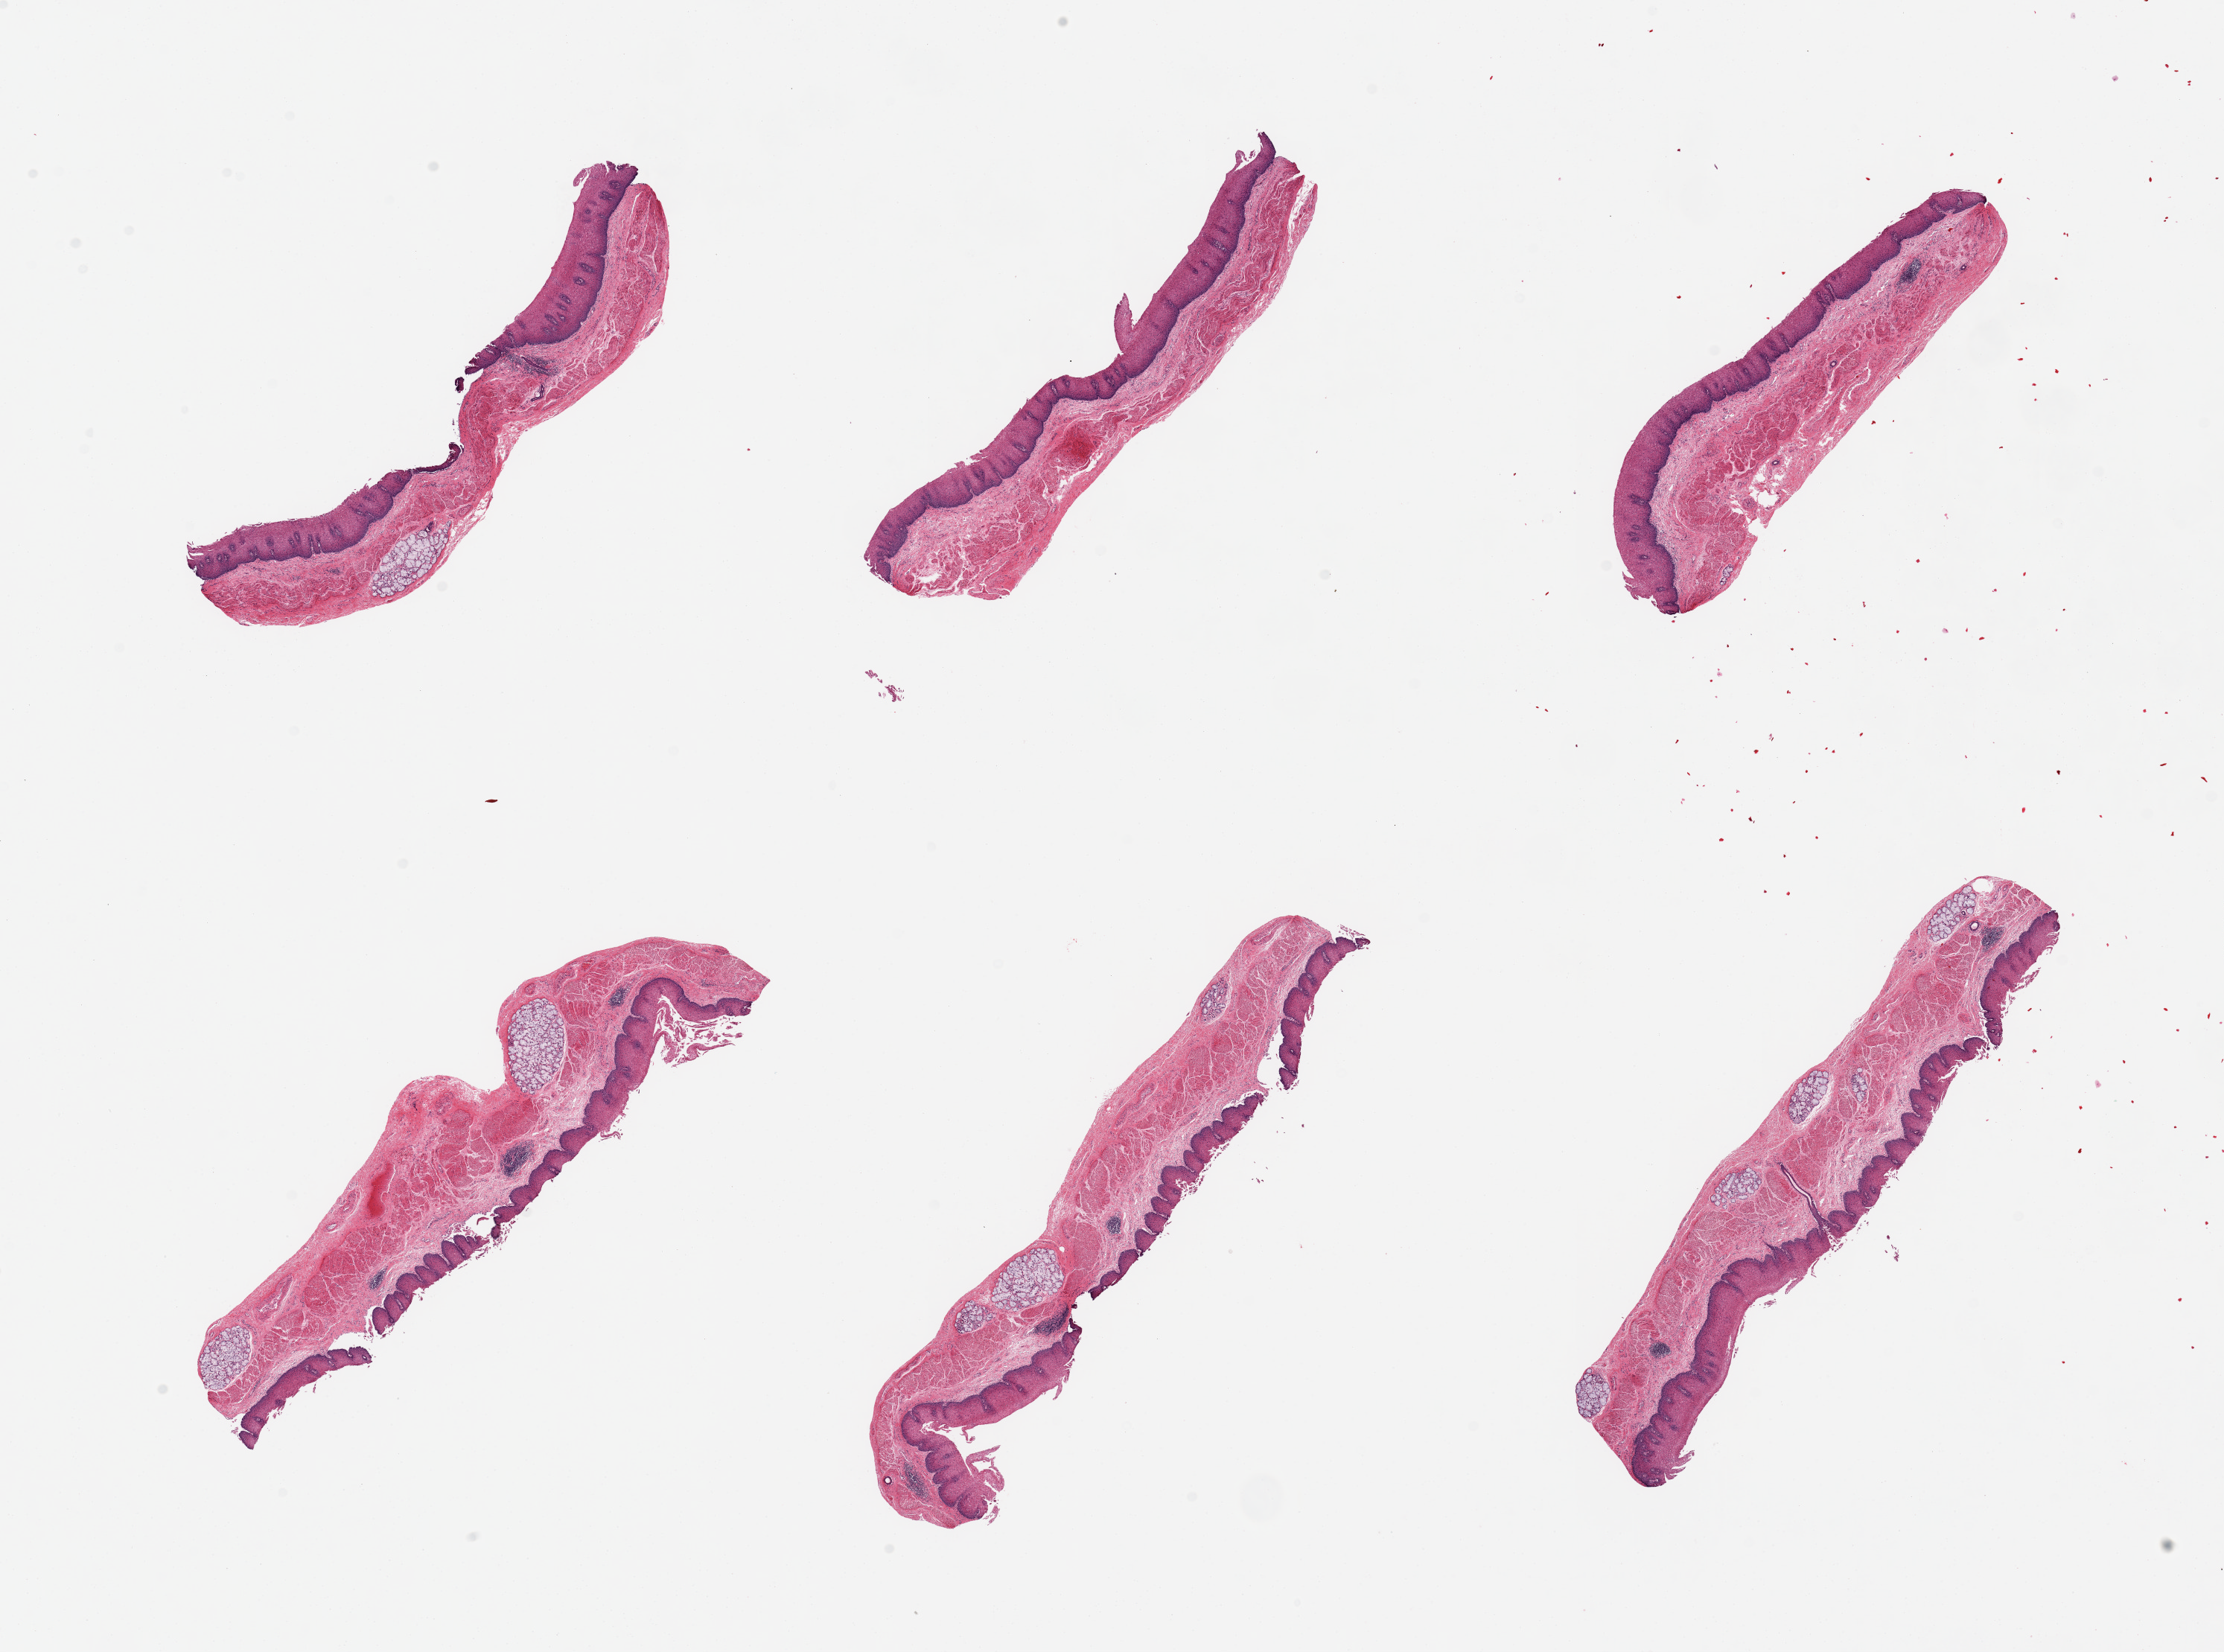
Haematoxylin and eosin whole-slide image — shown as a low-resolution overview of the whole scanned area (about 23.6 x 17.6 mm, from a 20x scan); PAXgene-fixed paraffin-embedded (PFPE) section; target tissue: esophageal mucous membrane; tissue donor sample. Male donor.
* reviewer comment on this tissue sample: 6 pieces; 329um thick squamous epithelium, several clusters of submucosal glands